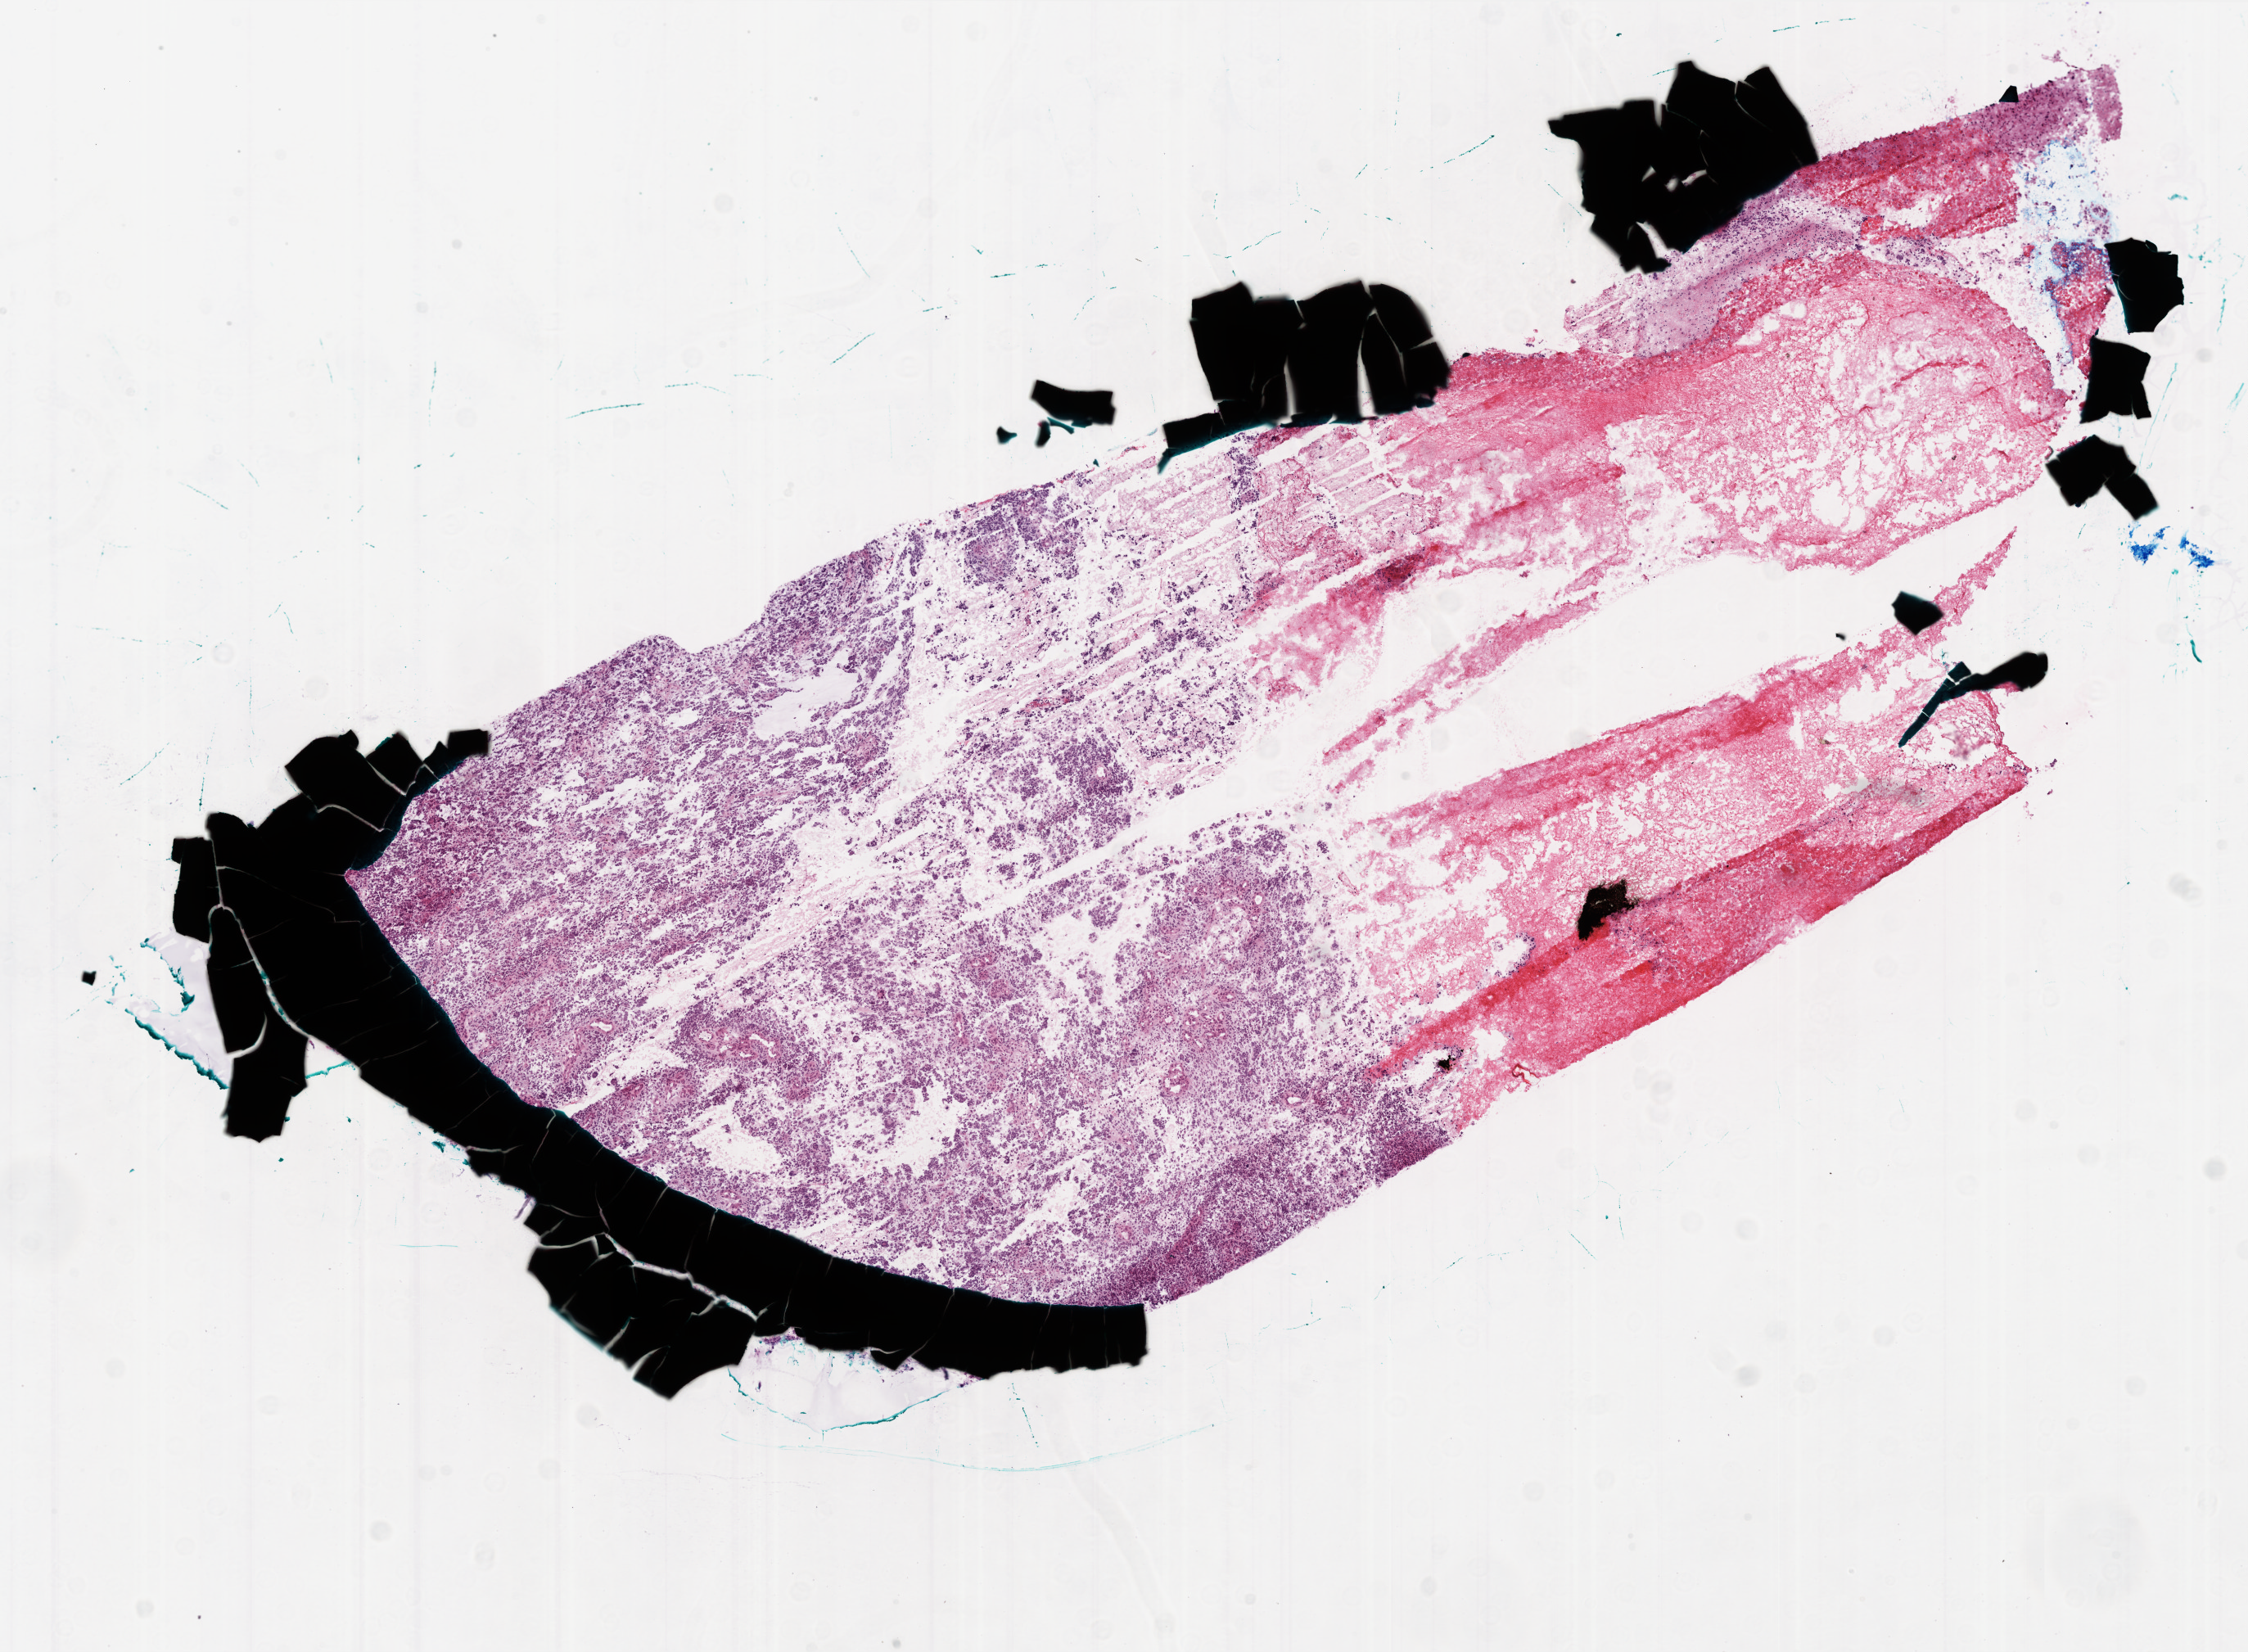
H&E-stained whole-slide image — whole scanned area (about 11.0 x 8.1 mm, acquisition: 20x scan) shown as a low-resolution overview; frozen section from the bottom of the tissue portion; primary tumour sample from the brain. Female, age 33 years at initial diagnosis. Composition of this section per pathologist review: tumour cells 80%, tumour nuclei 100%, normal cells 0%, stromal cells 0%, necrosis 20%. Inflammatory infiltration, as recorded: lymphocyte infiltration 0%, monocyte infiltration 0%, neutrophil infiltration 0%.
Pathologic diagnosis: Glioblastoma.